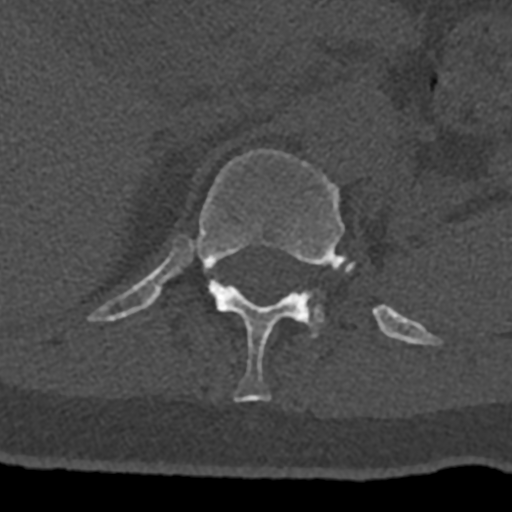
CT including the spine, one axial slice; slice 486 of 797 in the series (ordered by position); 120 kVp; bone window (W 1800 / L 400 HU); 0.5 mm slice thickness; 512 × 512 image matrix. Patient: male, 74 years. Case-level facts recorded for this patient, not image findings: primary cancer: renal.
Structures marked on this image (semi-automatic segmentation, software-assisted and operator-edited):
- L1 vertebra: bounding box <306,293,324,337> (left, top, right, bottom; pixels)
- T12 vertebra: <87,149,432,402>